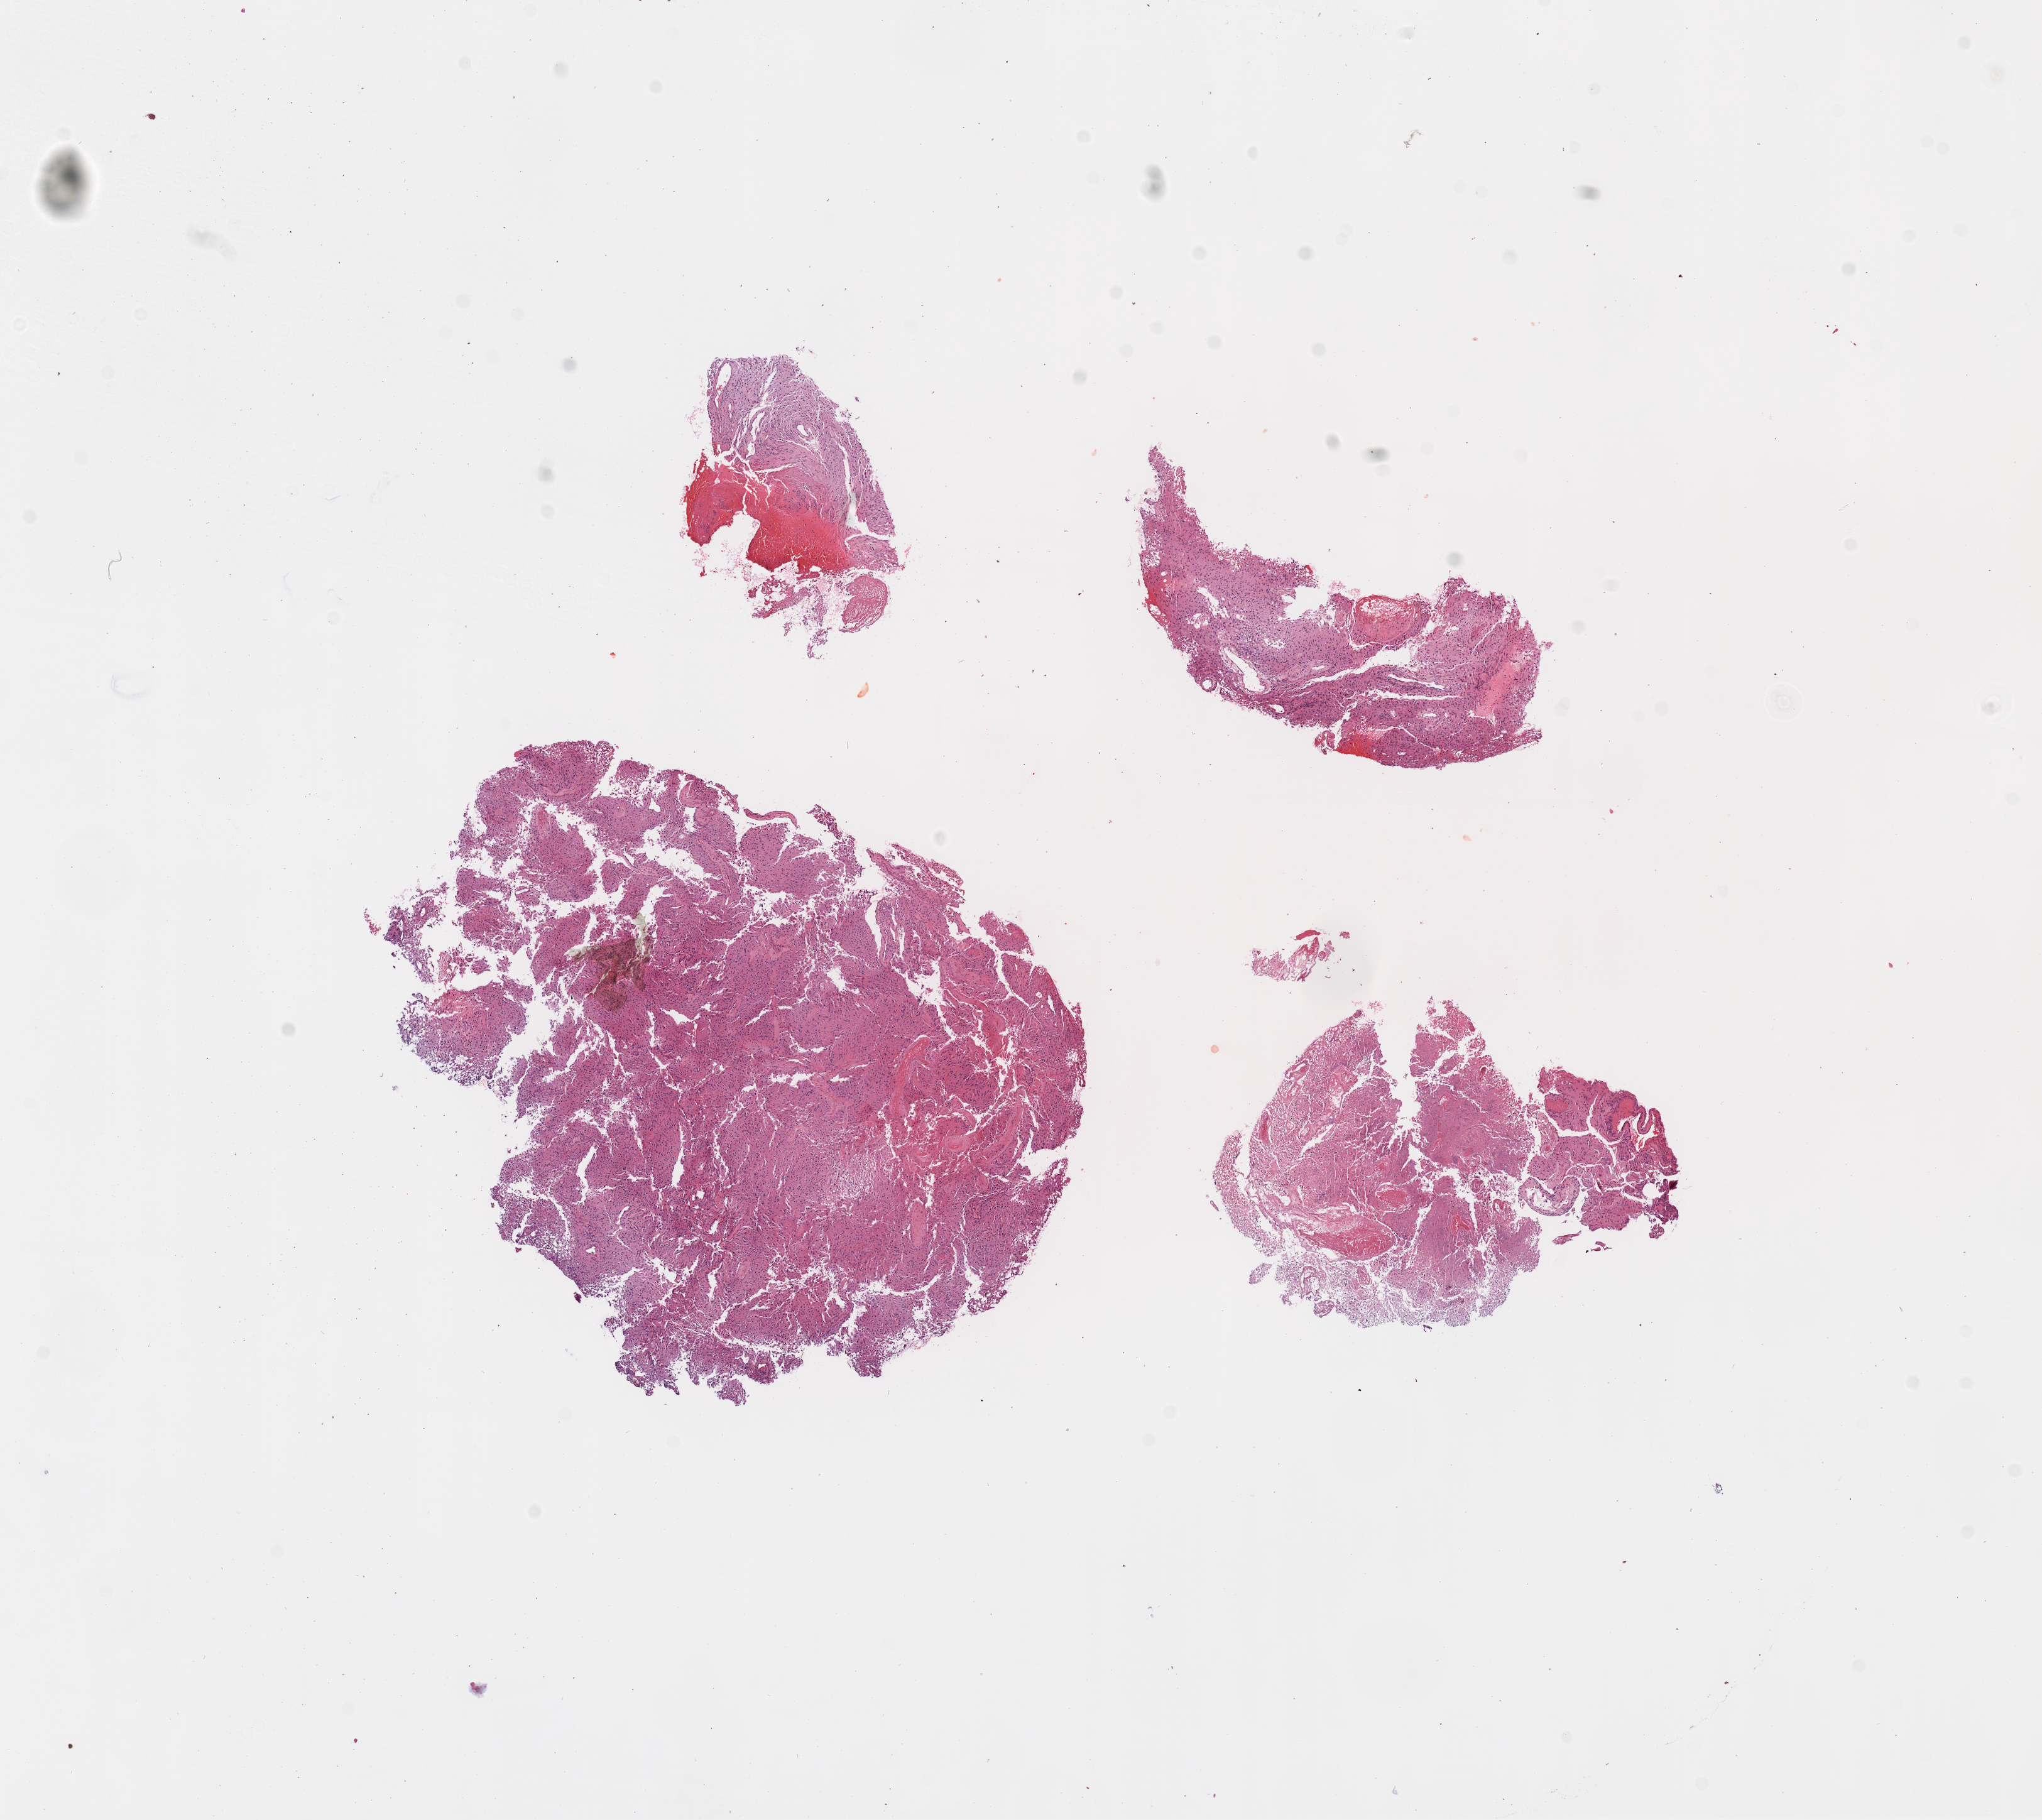
Hematoxylin and eosin (H&E) stained whole-slide image — shown as a low-resolution overview of the whole scanned area (about 13.0 x 11.6 mm, from a 20x scan); formalin-fixed paraffin-embedded (FFPE) diagnostic section; primary tumour sample from the brain. Patient: male, age at initial diagnosis 55 years.
Pathologic diagnosis: Glioblastoma.